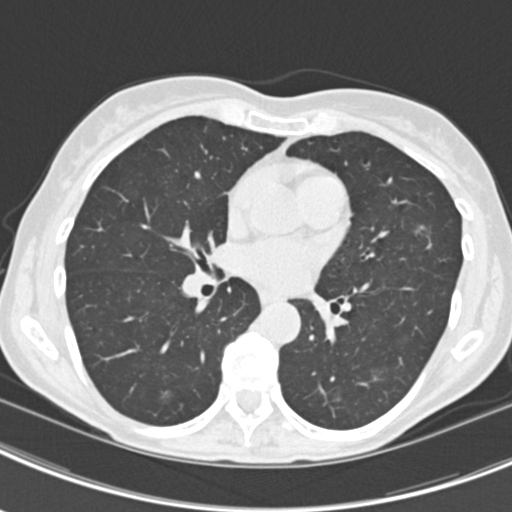
Chest CT (low-dose screening protocol), one axial image; second annual screen; lung window (W 1500 / L -600 HU); 2 mm slice thickness; standard (soft-tissue) reconstruction kernel (B30f); 120 kVp; slice 97 of 219 in the series; 512 × 512 image matrix. Female, age 63 years at enrolment.
• Lesion marked by an expert reader, bounding box <400,210,437,253> (left, top, right, bottom; pixels).
• The screening reader recorded 9 non-calcified nodules or masses ≥4 mm on this exam; which of them this box marks is not recorded.
• Official screen result: positive, other.
• Participant outcome: lung cancer diagnosed 408 days after this screen (after the third annual screen) — bronchiolo-alveolar adenocarcinoma, NOS, right upper lobe, right middle lobe, right lower lobe, left upper lobe, left lower lobe, moderately differentiated (G2), stage IV (AJCC 6th edition).